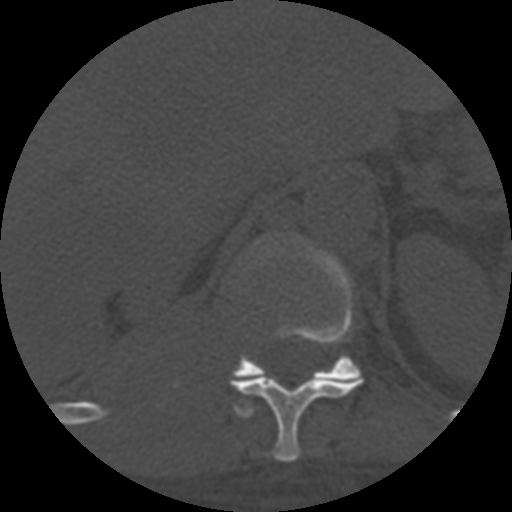
CT including the spine, one axial slice; position 326 of 708 along the scan axis; reconstruction kernel STANDARD; 120 kVp; one of 3 acquisitions stored at this slice position; bone window (W 1800 / L 400 HU); 1.25 mm slice thickness; 512 × 512 image matrix, field of view 160 × 160 mm. Patient age 55 years. Case-level facts recorded for this patient, not image findings: primary cancer: colon; vertebrae with lytic lesions (as recorded): T12, L1, L5.
Structures marked on this image (semi-automatic segmentation, software-assisted and operator-edited):
- T11 vertebra: box from (x=230, y=252) to (x=363, y=462) px
- T12 vertebra: (x=232, y=243)–(x=362, y=381)